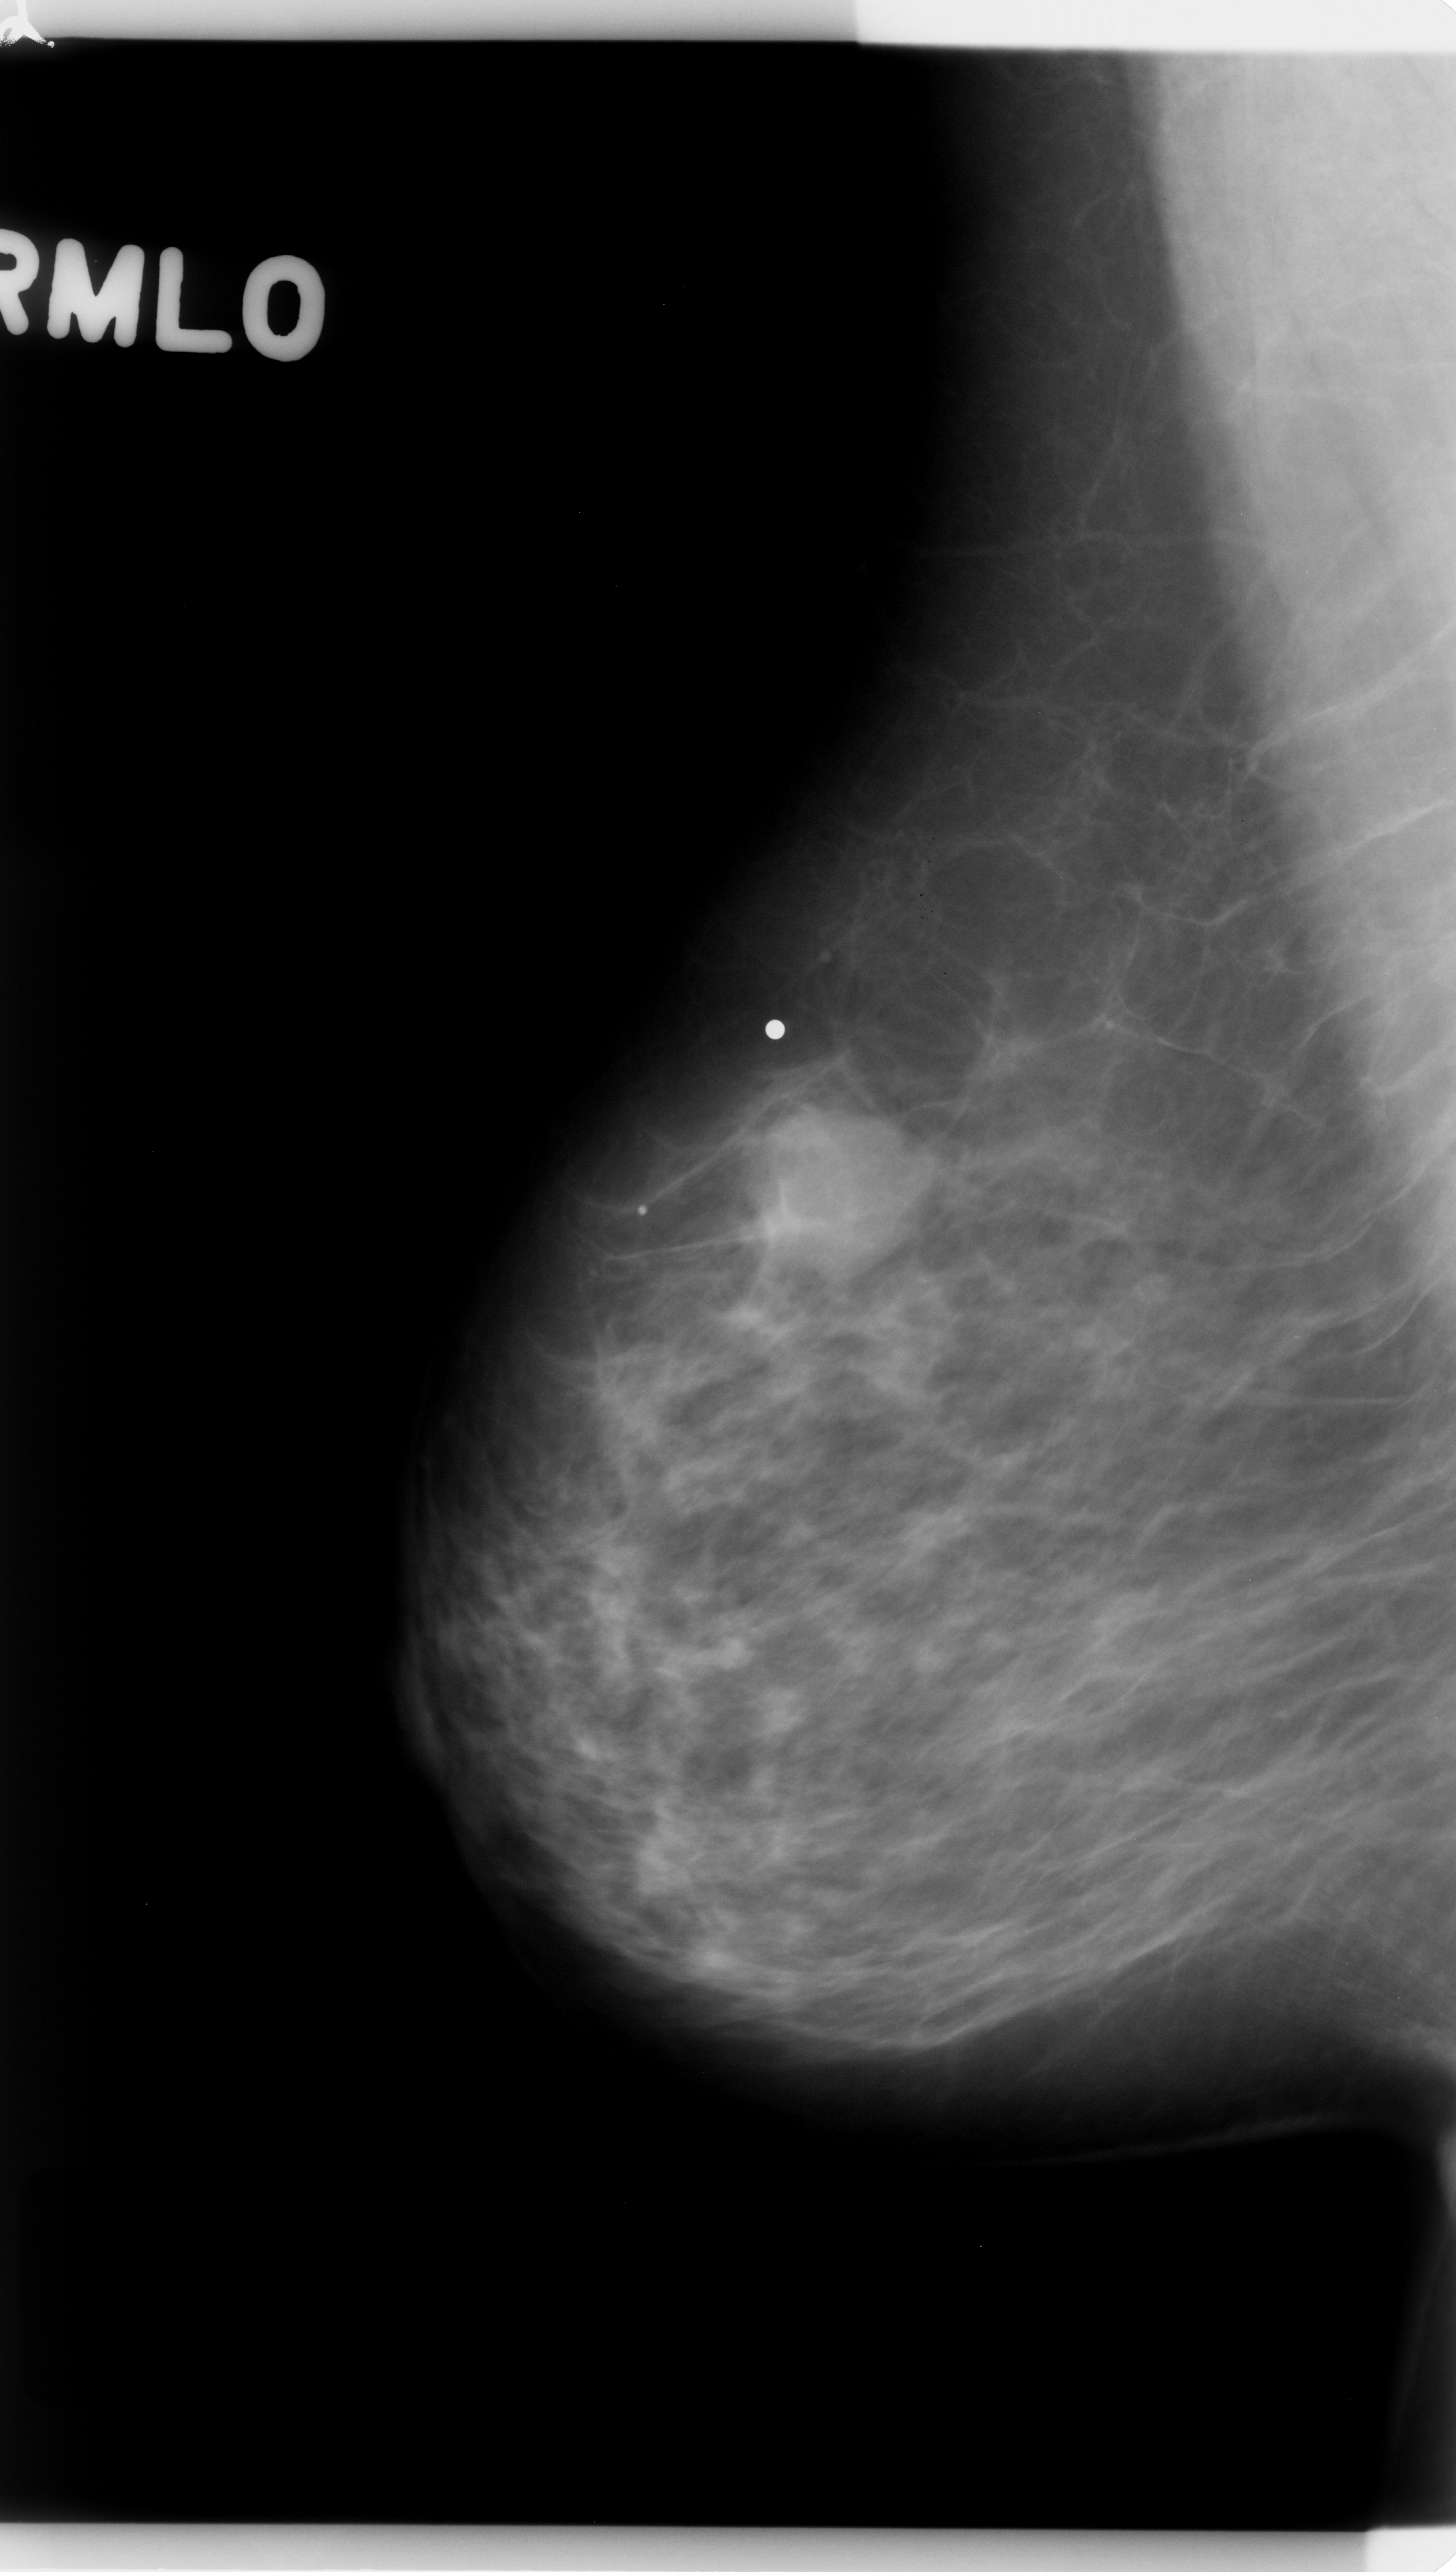
Mammogram (digitized film); right breast; MLO view; breast composition: scattered fibroglandular densities (BI-RADS density category 2 of 4); 1456 × 2572 image matrix.
Expert-marked regions of interest on this image (one box per marked abnormality):
- mass, shape round, margins microlobulated; BI-RADS assessment category 4; subtlety rating 5 on a 1 (subtle) to 5 (obvious) scale; pathology result (as recorded, not read from the image): benign: bounding box (x1, y1, x2, y2) in pixels: (748, 1102, 924, 1282)